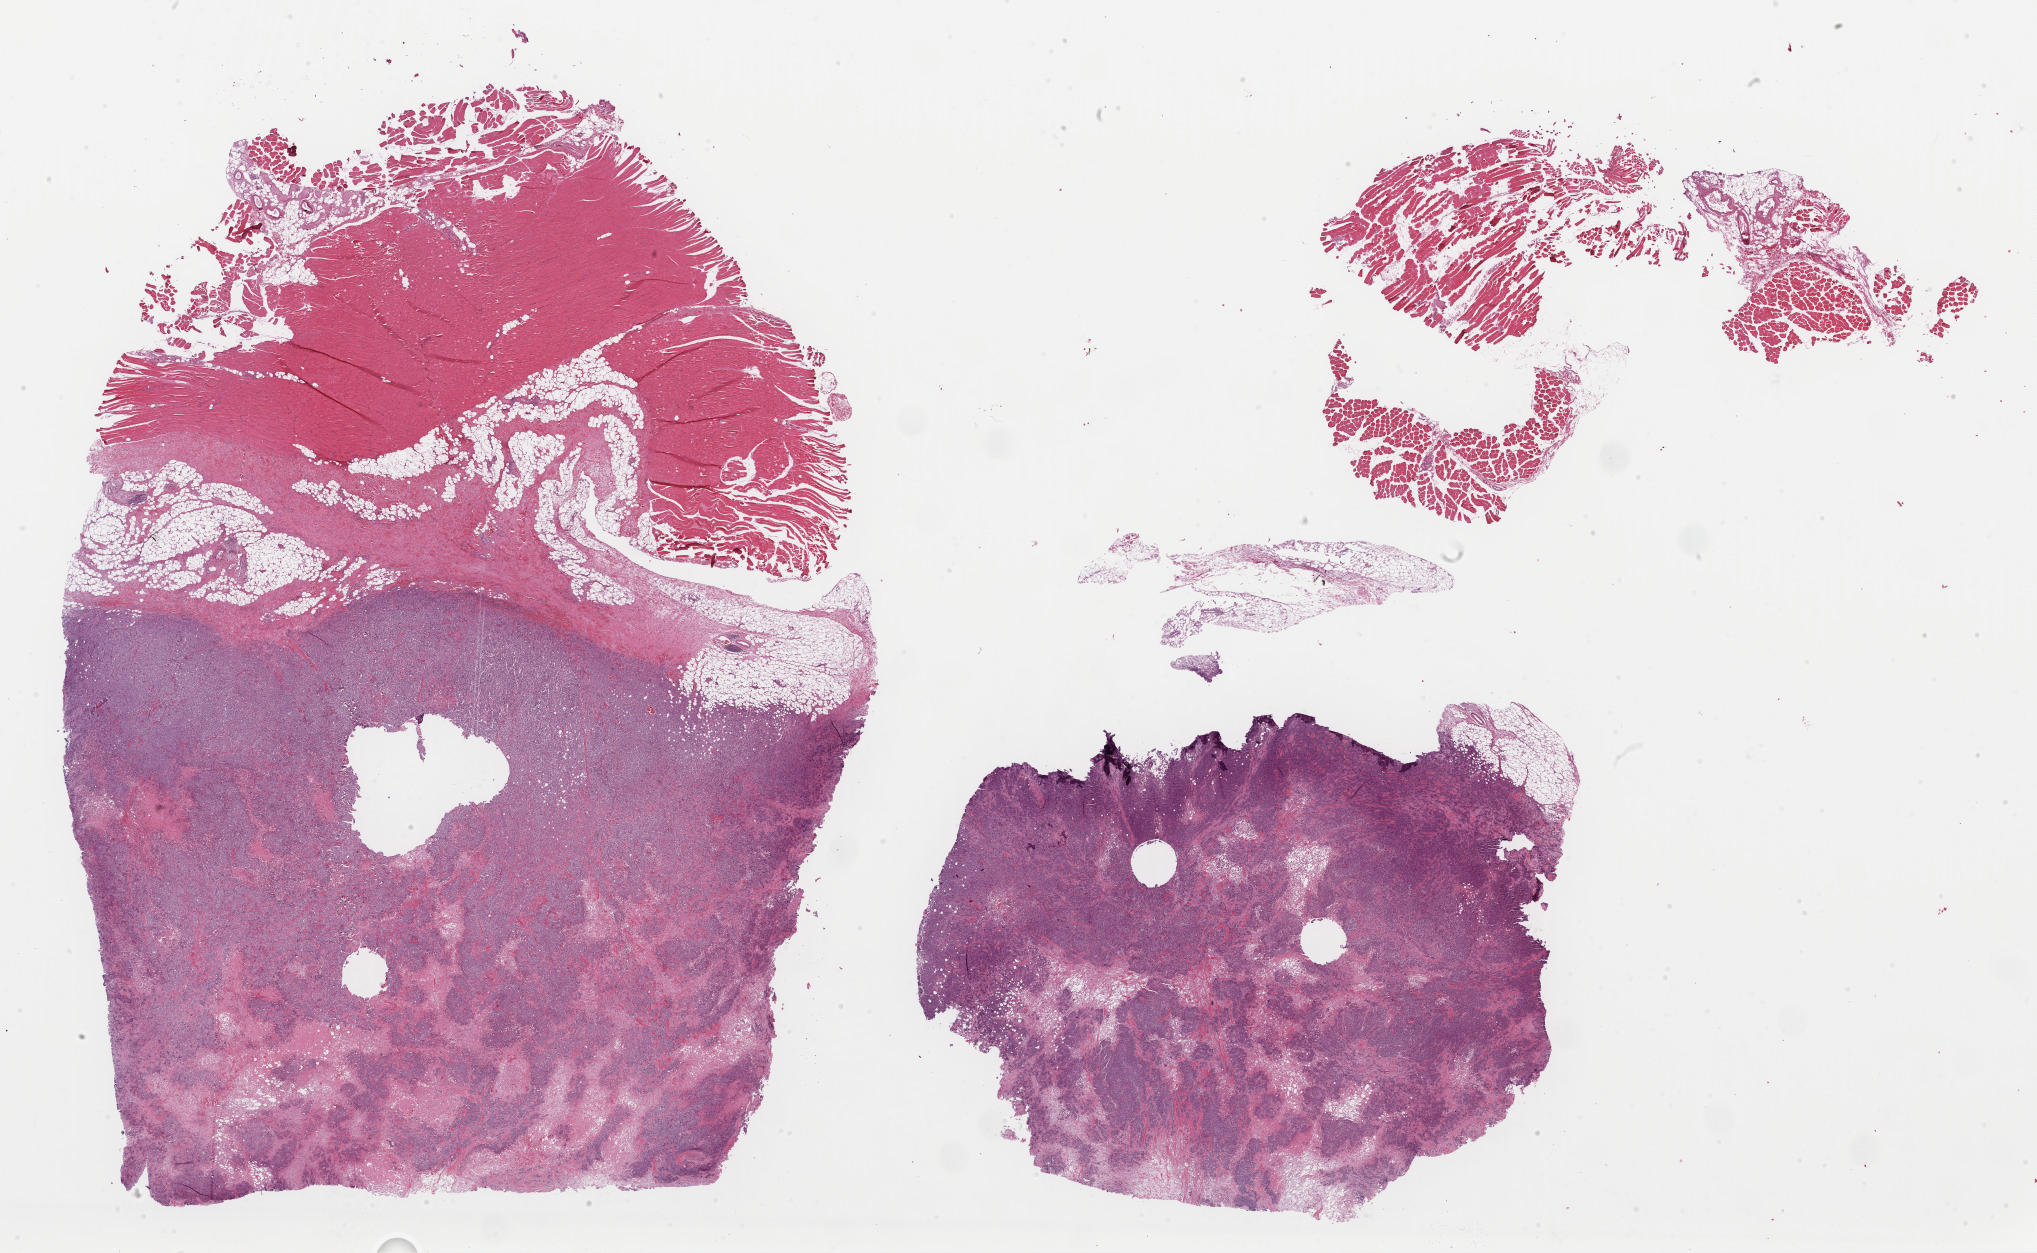
Digitized Hematoxylin and eosin (H&E) stained tissue section (whole slide), shown as a low-resolution overview of the whole scanned area (about 32.2 x 19.8 mm), formalin-fixed paraffin-embedded (FFPE) diagnostic section, primary tumour sample from the breast. Female patient; age at initial diagnosis 51 years.
TNM: T2 N1 M0. Lymph nodes positive (case pathology): 1 of 9 examined. AJCC pathologic stage: IIB. Pathologic diagnosis: Infiltrating duct carcinoma, NOS.